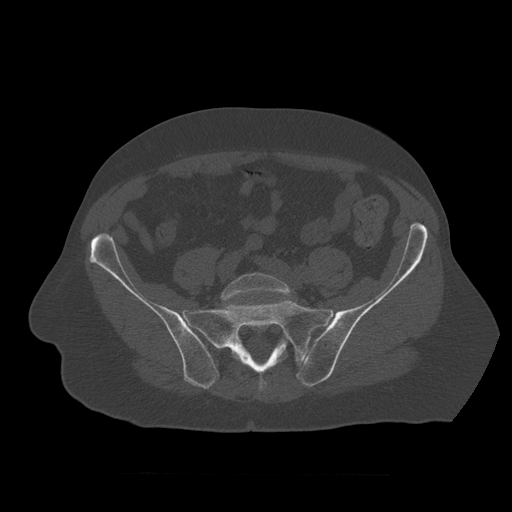
CT including the spine, one axial slice; slice 238 of 450 in the series (ordered by position); reconstruction kernel STANDARD; 120 kVp; bone window (W 1800 / L 400 HU); 512 × 512 image matrix, field of view 405 × 405 mm. Patient age 75 years. Case-level facts recorded for this patient, not image findings: primary cancer: prostate.
Annotated regions visible in this slice (semi-automatic segmentation, software-assisted and operator-edited):
- L5 vertebra: bounding box <221,273,294,301> (left, top, right, bottom; pixels)